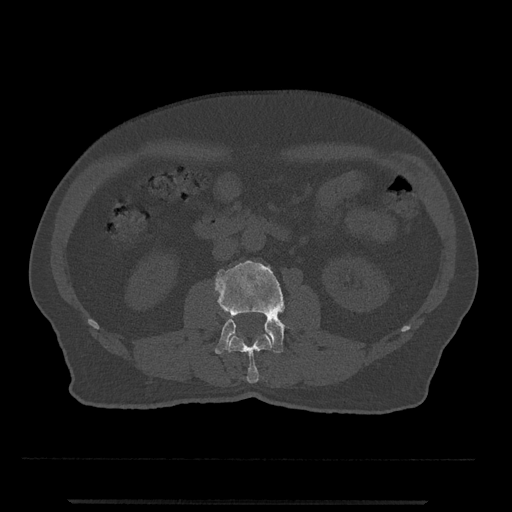
CT including the spine, one axial slice; slice 228 of 797 in the series (ordered by position); reconstruction kernel Br40s/3; 120 kVp; bone window (W 1800 / L 400 HU); 0.5 mm slice thickness; 512 × 512 image matrix, field of view 419 × 419 mm. Male patient, age 63 years. From the clinical record (not read from this slice): primary cancer: prostate.
Outlined on this slice (semi-automatic segmentation, software-assisted and operator-edited):
- L2 vertebra: box from (x=227, y=333) to (x=273, y=383) px
- L3 vertebra: (x=214, y=260)–(x=285, y=354)